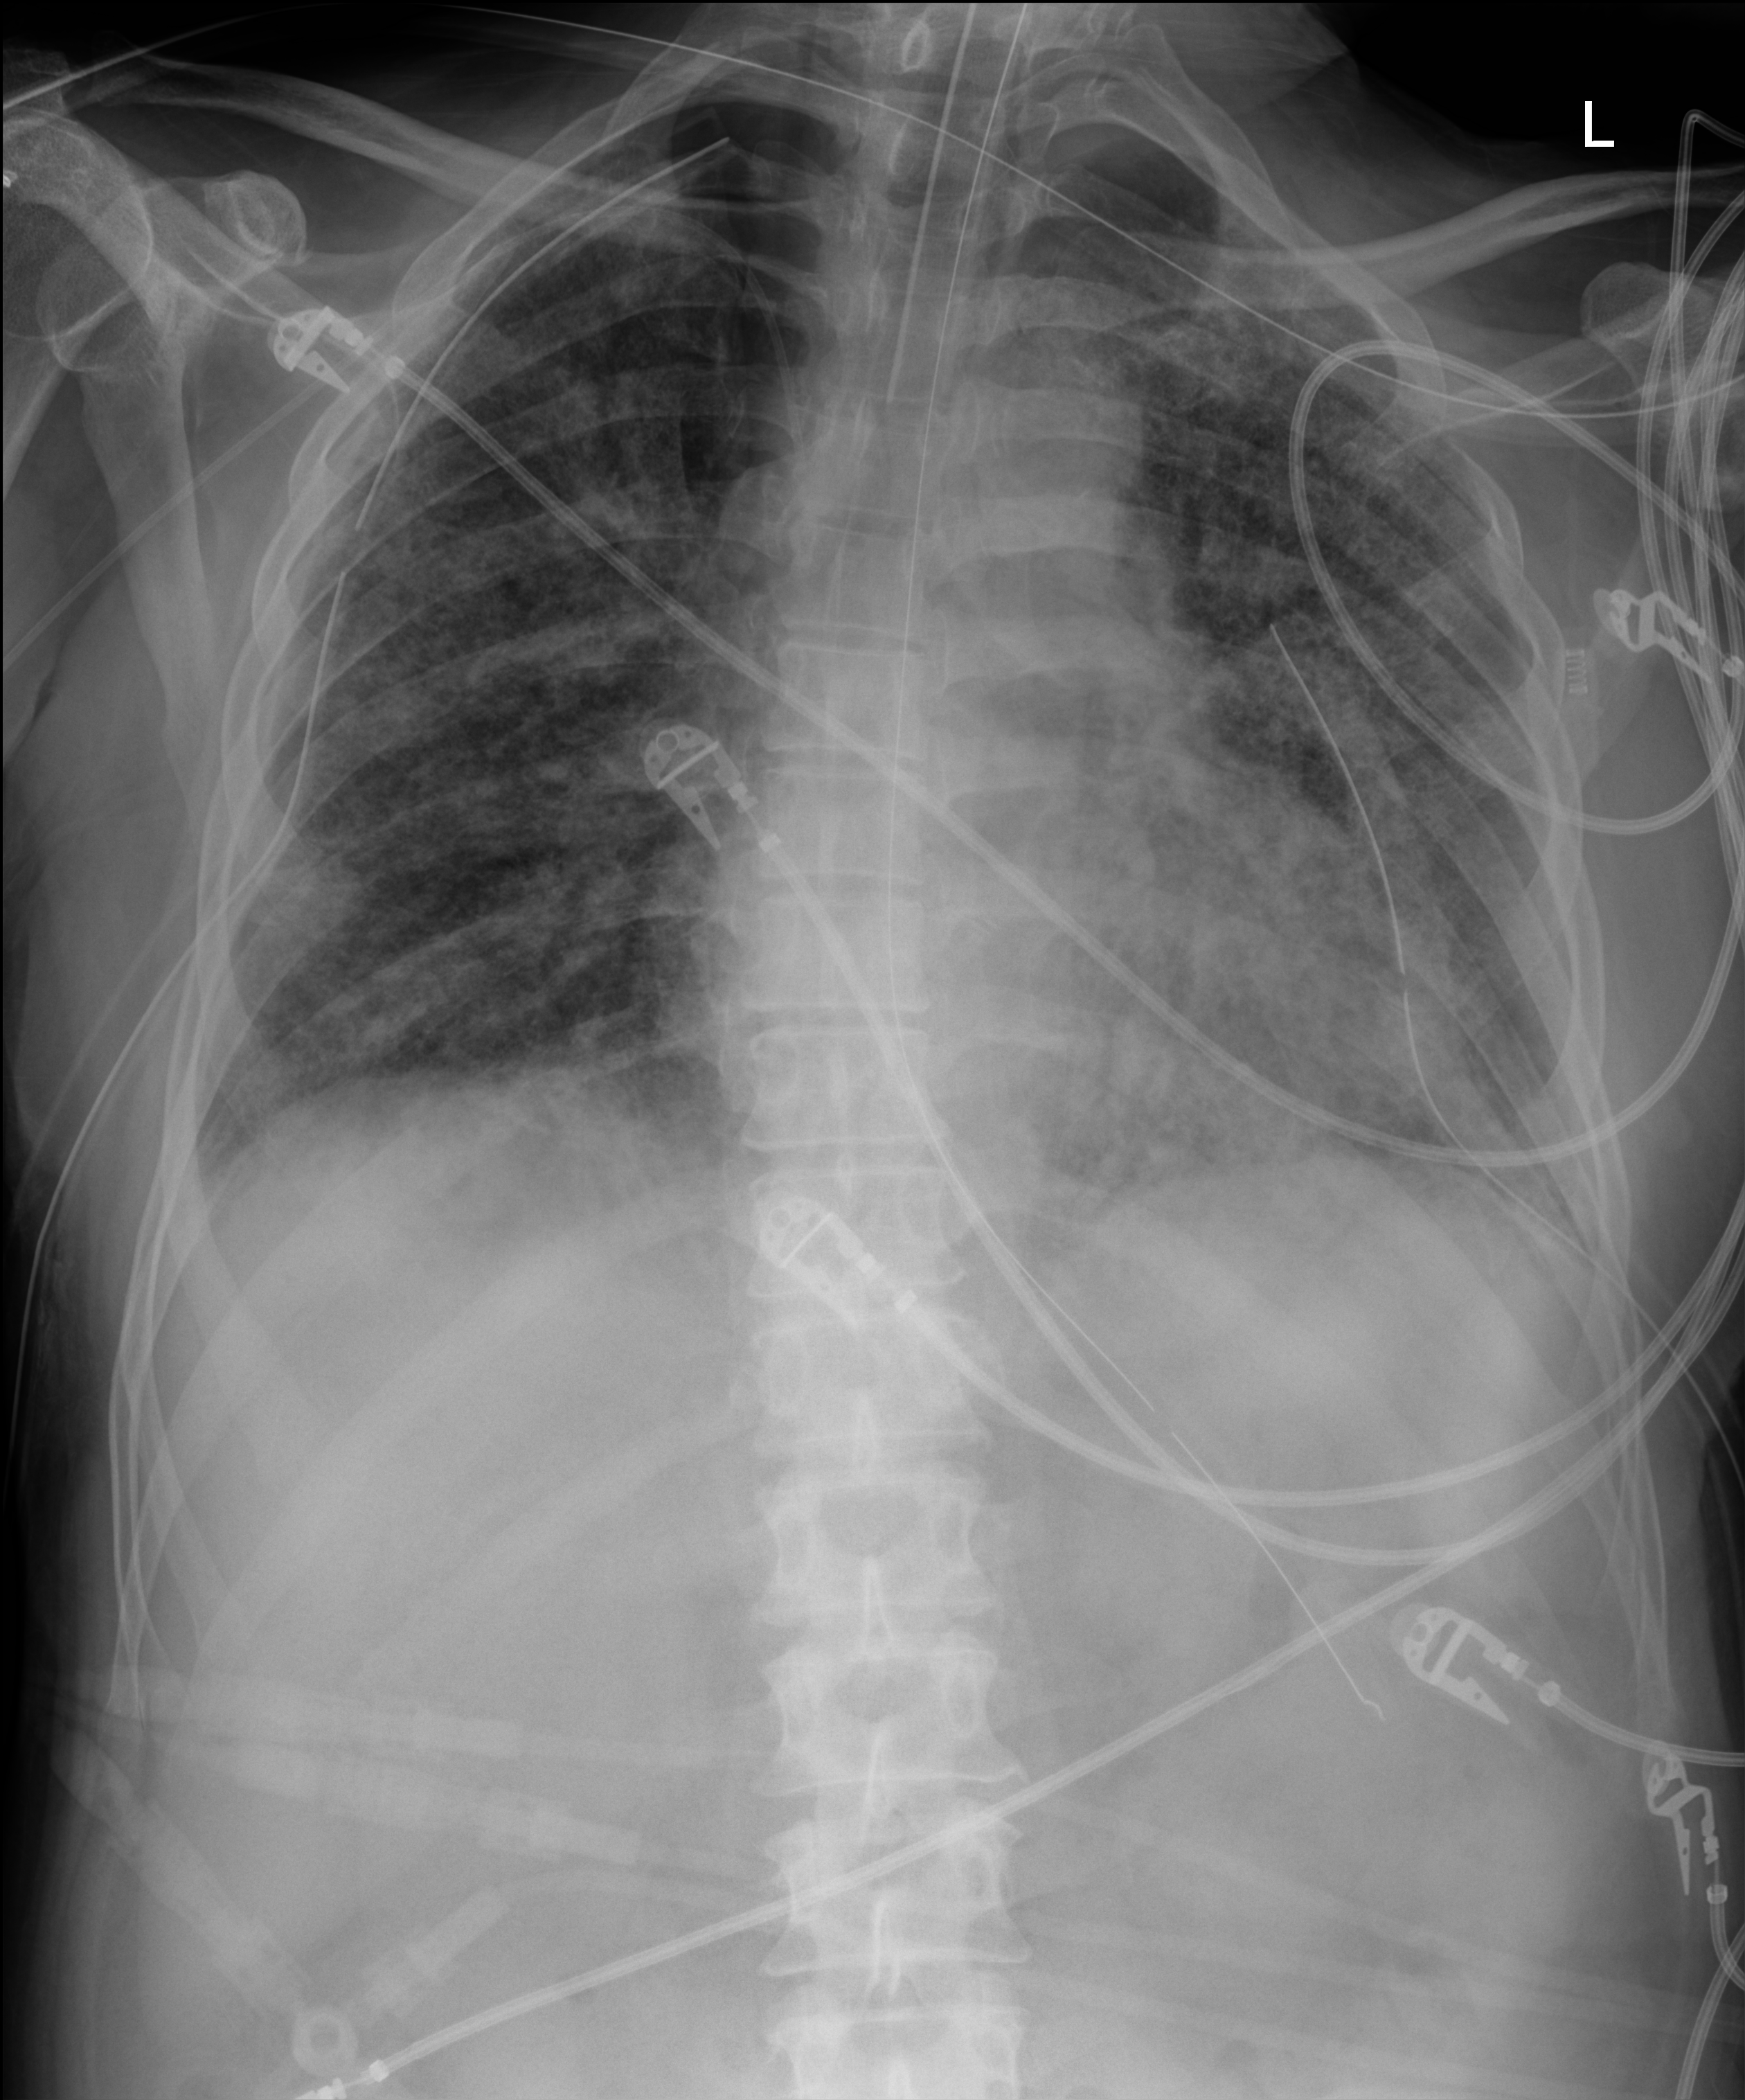
Chest X-ray. Male patient hospitalised with COVID-19, age 60–74 years.
Admission-level facts for this patient (not findings on this image; timing relative to this image not recorded): mechanically ventilated during this hospital stay: yes.